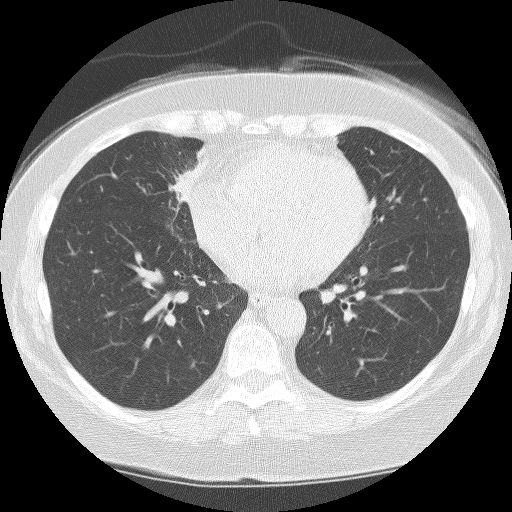
Low-dose screening chest CT, one axial slice. Position 75 of 159 along the scan axis. Reconstruction kernel BONE. Lung window (W 1500 / L -600 HU). 2.5 mm slice thickness. 512 × 512 image matrix, field of view 299 × 299 mm.
Annotated regions visible in this slice (expert manual segmentation):
- lesion 1 (tumor, hilum of right lung): box from (x=167, y=145) to (x=208, y=203) px